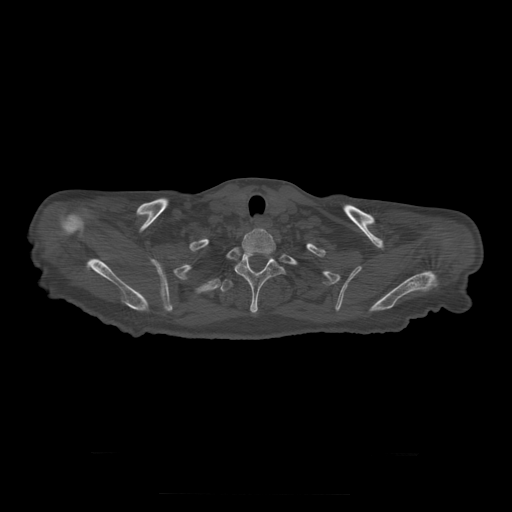
CT including the spine, one axial slice. Position 276 of 397 along the scan axis. 120 kVp. Bone window (W 1800 / L 400 HU). 512 × 512 image matrix, field of view 510 × 510 mm. Patient age 73 years. From the clinical record (not read from this slice): primary cancer: prostate.
Structures marked on this image (semi-automatically segmented with operator editing):
- T1 vertebra: bounding box (x1, y1, x2, y2) in pixels: (242, 231, 276, 255)
- T2 vertebra: (235, 253, 286, 314)
- T3 vertebra: (220, 280, 234, 292)